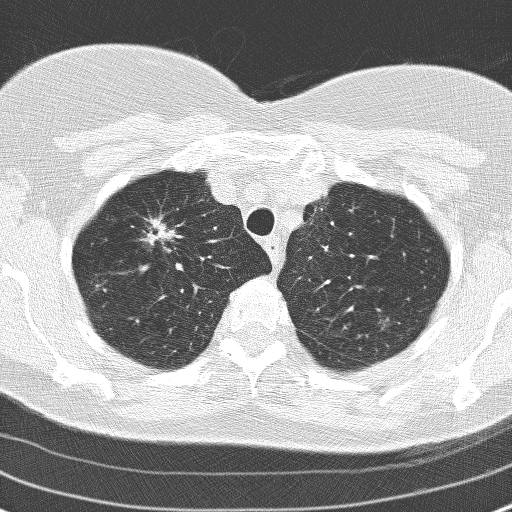
Low-dose screening chest CT, one axial slice. Position 129 of 160 along the scan axis. 120 kVp. Lung window (W 1500 / L -600 HU). 512 × 512 image matrix, field of view 313 × 313 mm.
Structures marked on this image (manually delineated by an expert):
- lesion 1 (tumor, upper lobe of right lung): box from (x=149, y=221) to (x=169, y=242) px